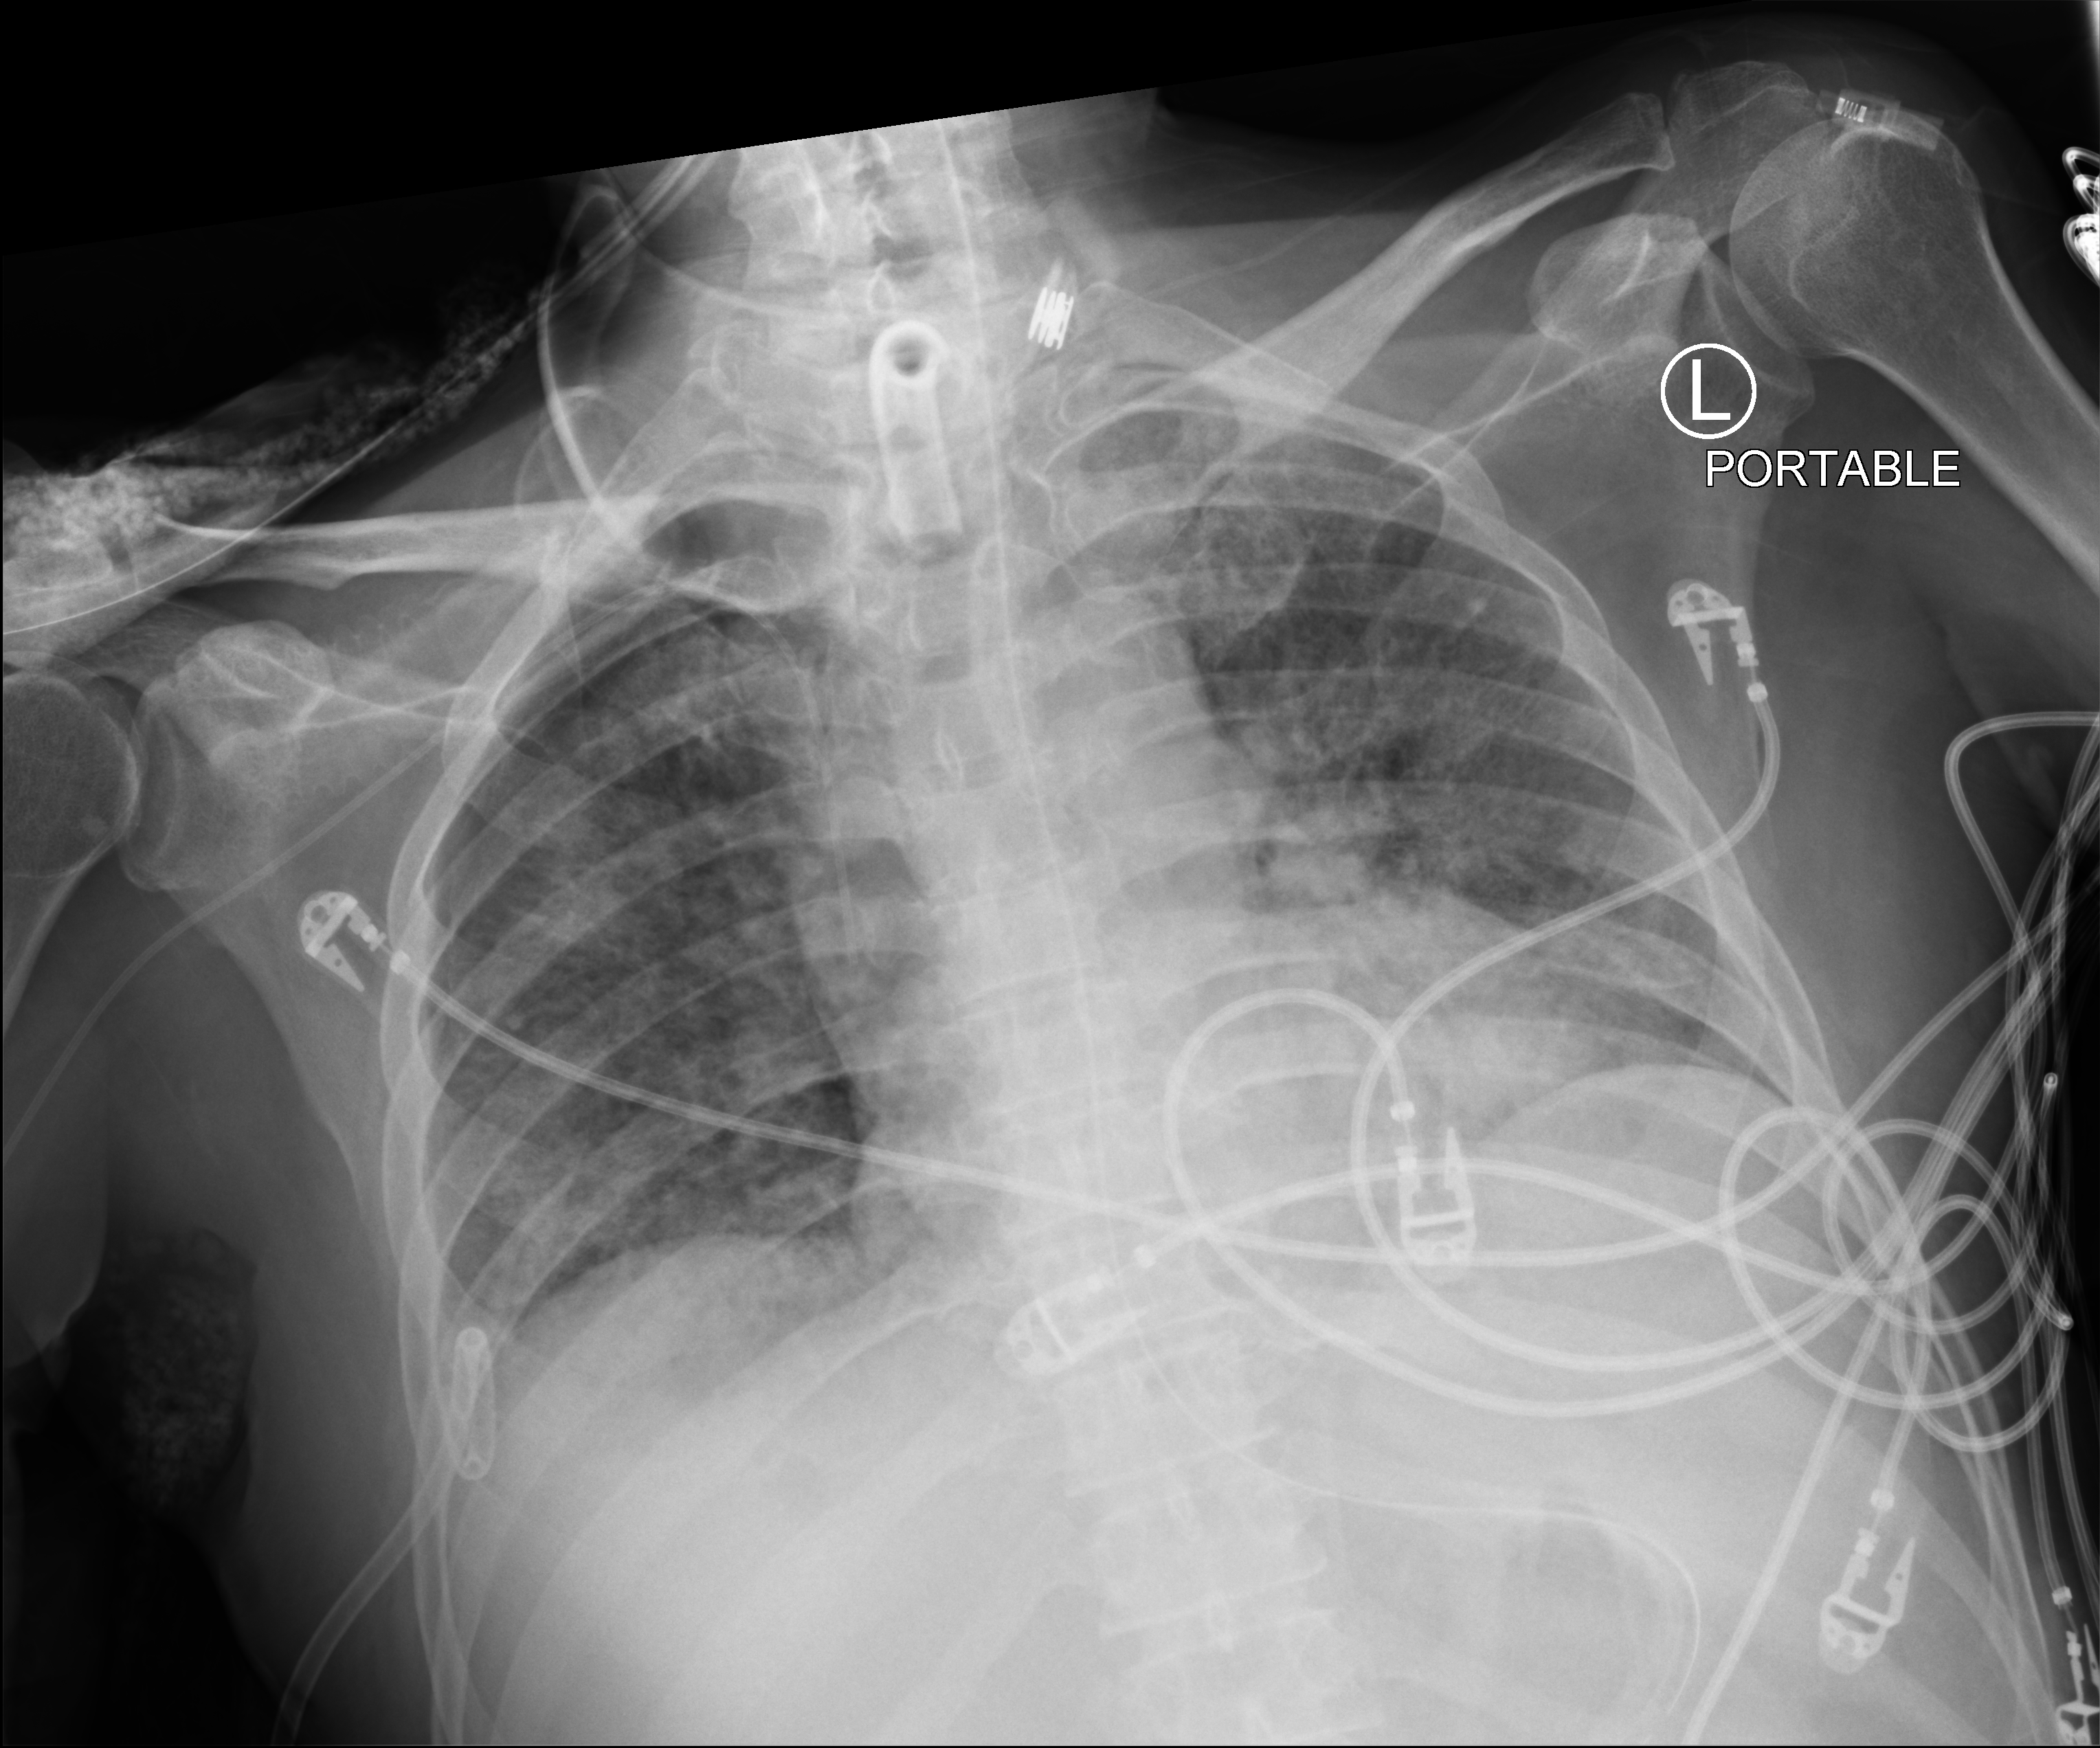
Chest X-ray (portable), anteroposterior (AP) projection. Male patient hospitalised with COVID-19, age 18–59 years.
Admission-level facts for this patient (not findings on this image; timing relative to this image not recorded): admitted to intensive care during this hospital stay: yes.